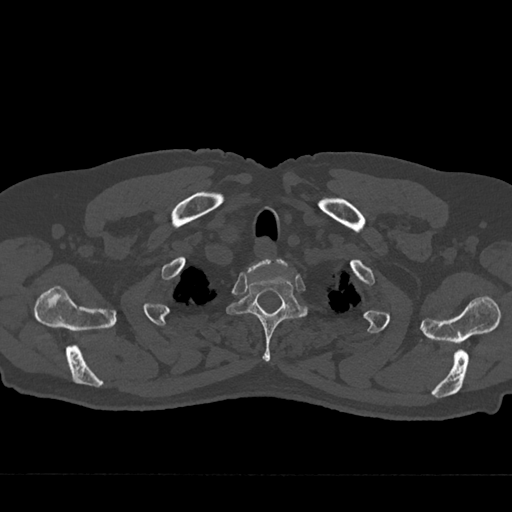
CT including the spine, one axial slice. Position 619 of 797 along the scan axis. 120 kVp. Bone window (W 1800 / L 400 HU). 512 × 512 image matrix. Male patient, age 75 years. From the clinical record (not read from this slice): primary cancer: renal; vertebrae with lytic lesions (as recorded): T4.
Annotated regions visible in this slice (semi-automatically segmented with operator editing):
- T1 vertebra: bounding box (x1, y1, x2, y2) in pixels: (248, 258, 288, 274)
- T2 vertebra: (226, 263, 308, 362)